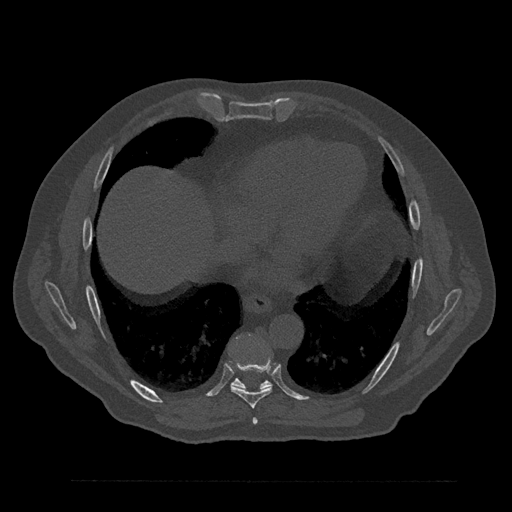
CT including the spine, one axial slice; slice 439 of 797 in the series (ordered by position); reconstruction kernel Br40s/3; 120 kVp; bone window (W 1800 / L 400 HU); 0.5 mm slice thickness; 512 × 512 image matrix, field of view 430 × 430 mm. Patient: male, 61 years. Case-level facts recorded for this patient, not image findings: primary cancer: prostate.
Annotated regions visible in this slice (semi-automatic segmentation, software-assisted and operator-edited):
- T7 vertebra: box from (x=252, y=418) to (x=258, y=425) px
- T8 vertebra: (x=230, y=358)–(x=272, y=408)
- T9 vertebra: (x=231, y=378)–(x=272, y=389)